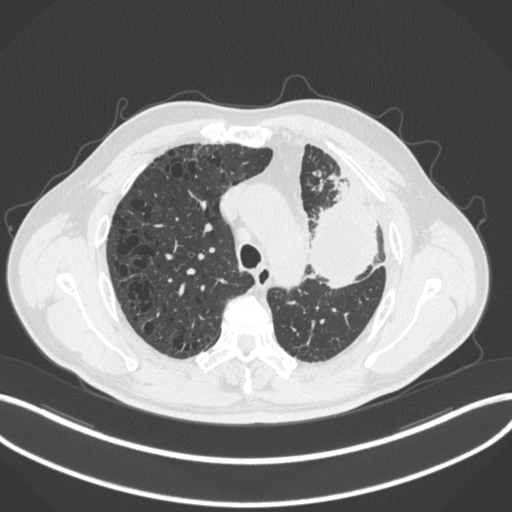
Chest CT, one axial slice; reconstruction kernel B31f; 120 kVp; lung window (W 1500 / L -600 HU); 1 mm slice thickness; 512 × 512 image matrix, field of view 400 × 400 mm. Male patient, age 68 years. Case-level facts recorded for this patient, not image findings: clinical TNM (as recorded): T3 N3 M1.
Structures marked on this image (rectangle marked by the reading radiologist):
- lung tumour (recorded histology: adenocarcinoma): box from (x=305, y=179) to (x=386, y=289) px